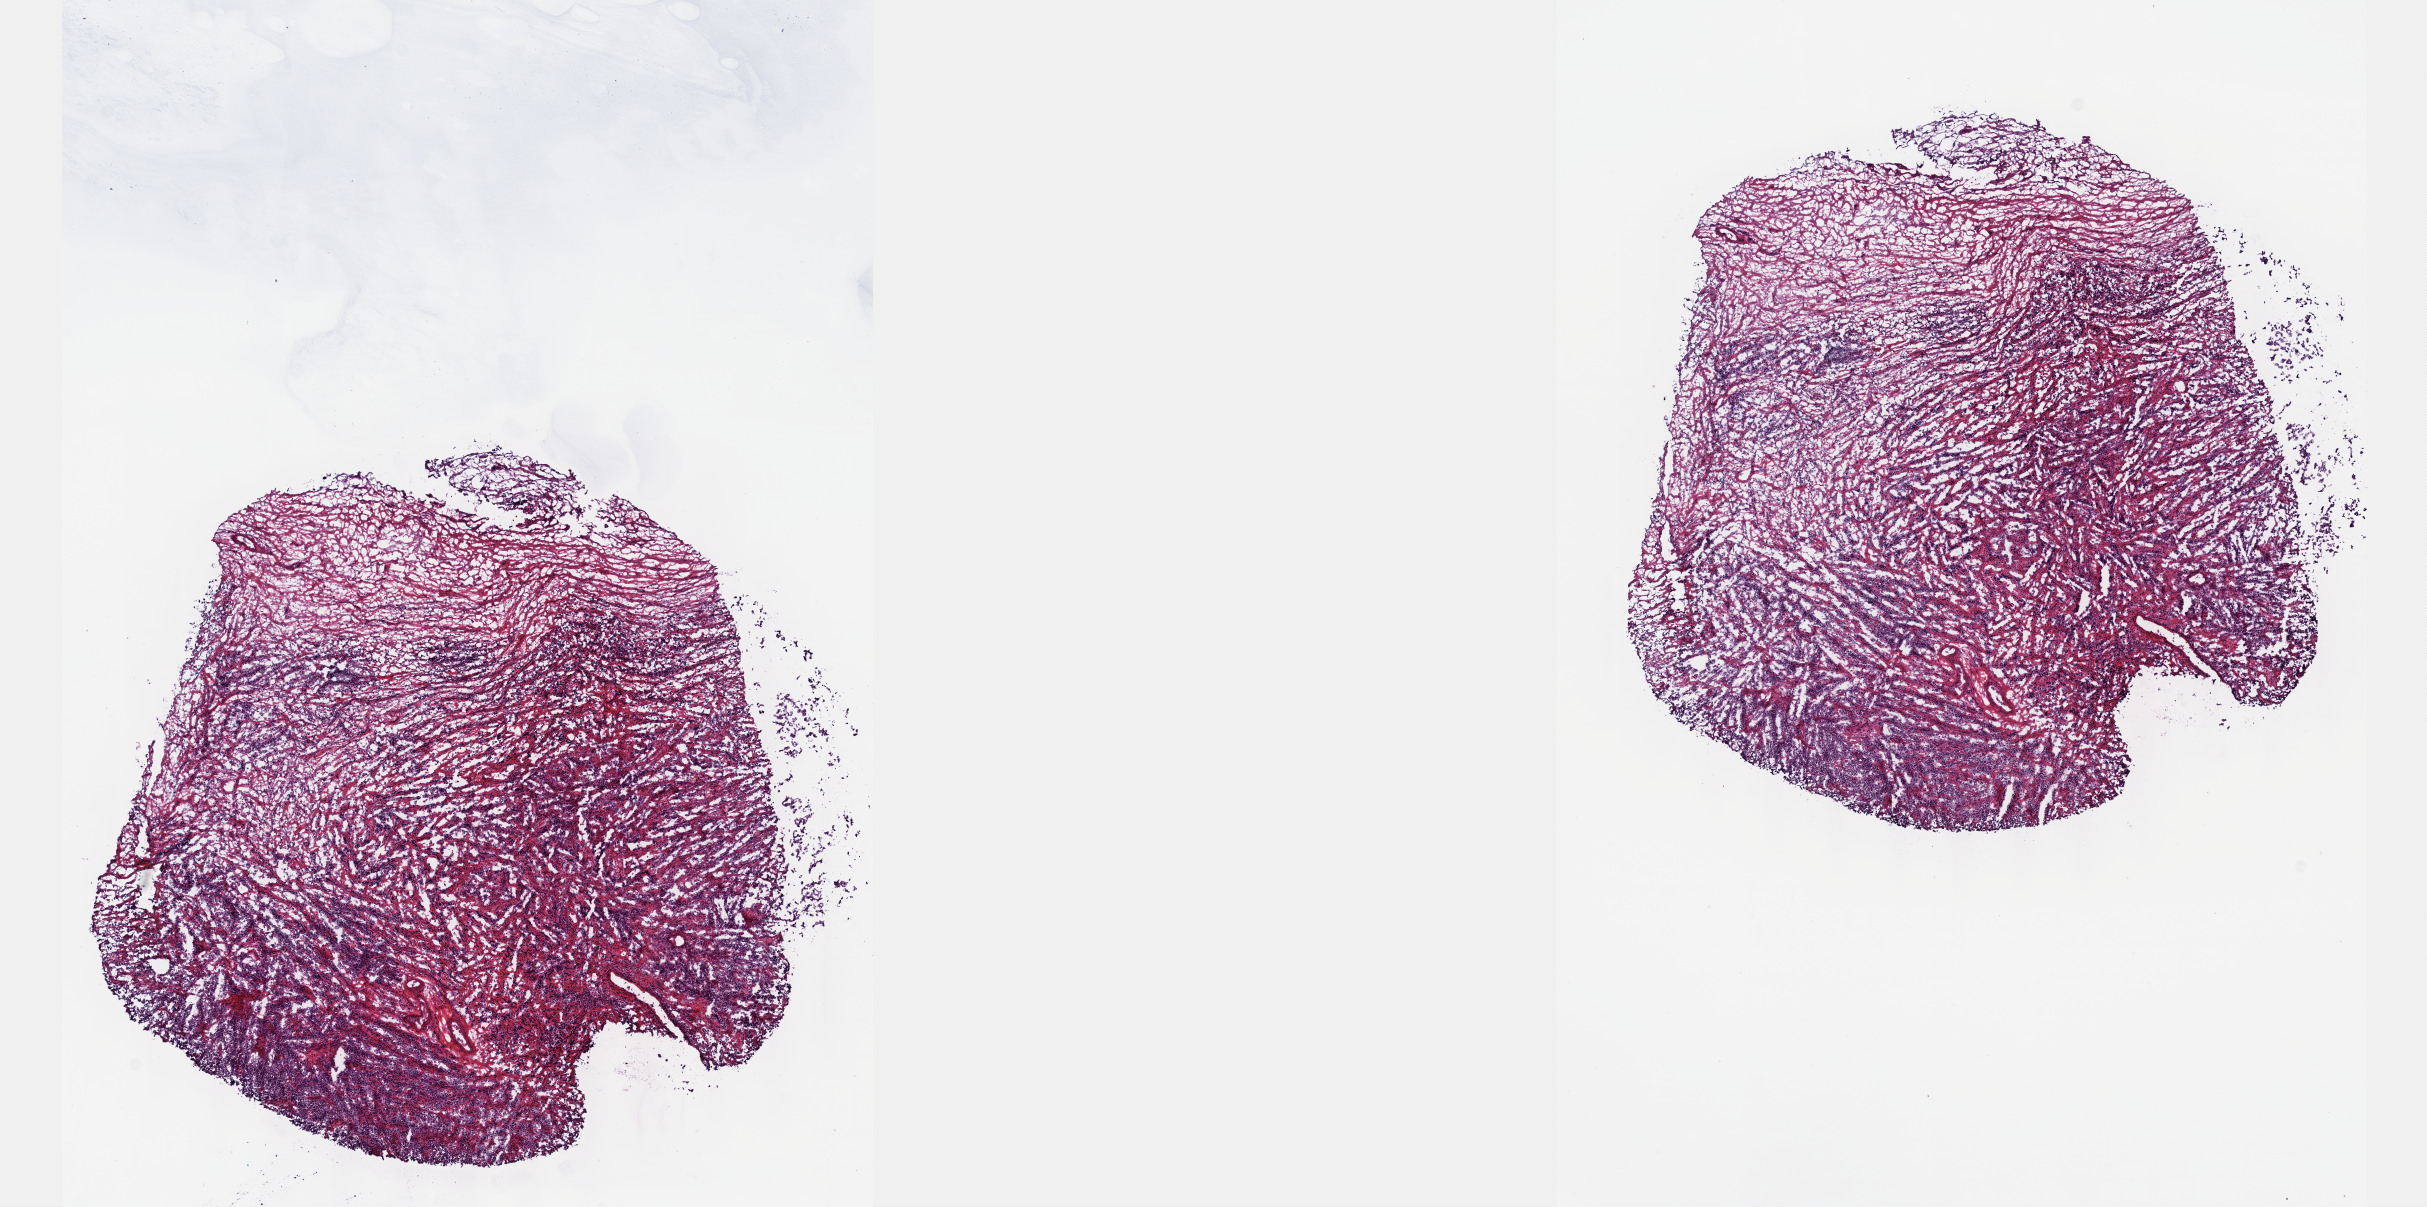
Whole-slide histology image, H&E-stained — whole scanned area (about 19.6 x 9.8 mm) shown as a low-resolution overview; frozen section from the top of the tissue portion; testis, primary tumour sample. Male, age 35 years at initial diagnosis. Composition of this section per pathologist review: tumour cells 100%, tumour nuclei 65%, normal cells 0%, stromal cells 0%, necrosis 0%. Infiltration values recorded for this section: lymphocyte infiltration 1%, monocyte infiltration 0%, neutrophil infiltration 0%.
Diagnosis: Seminoma, NOS. AJCC pathologic stage: IA. Laterality: right.